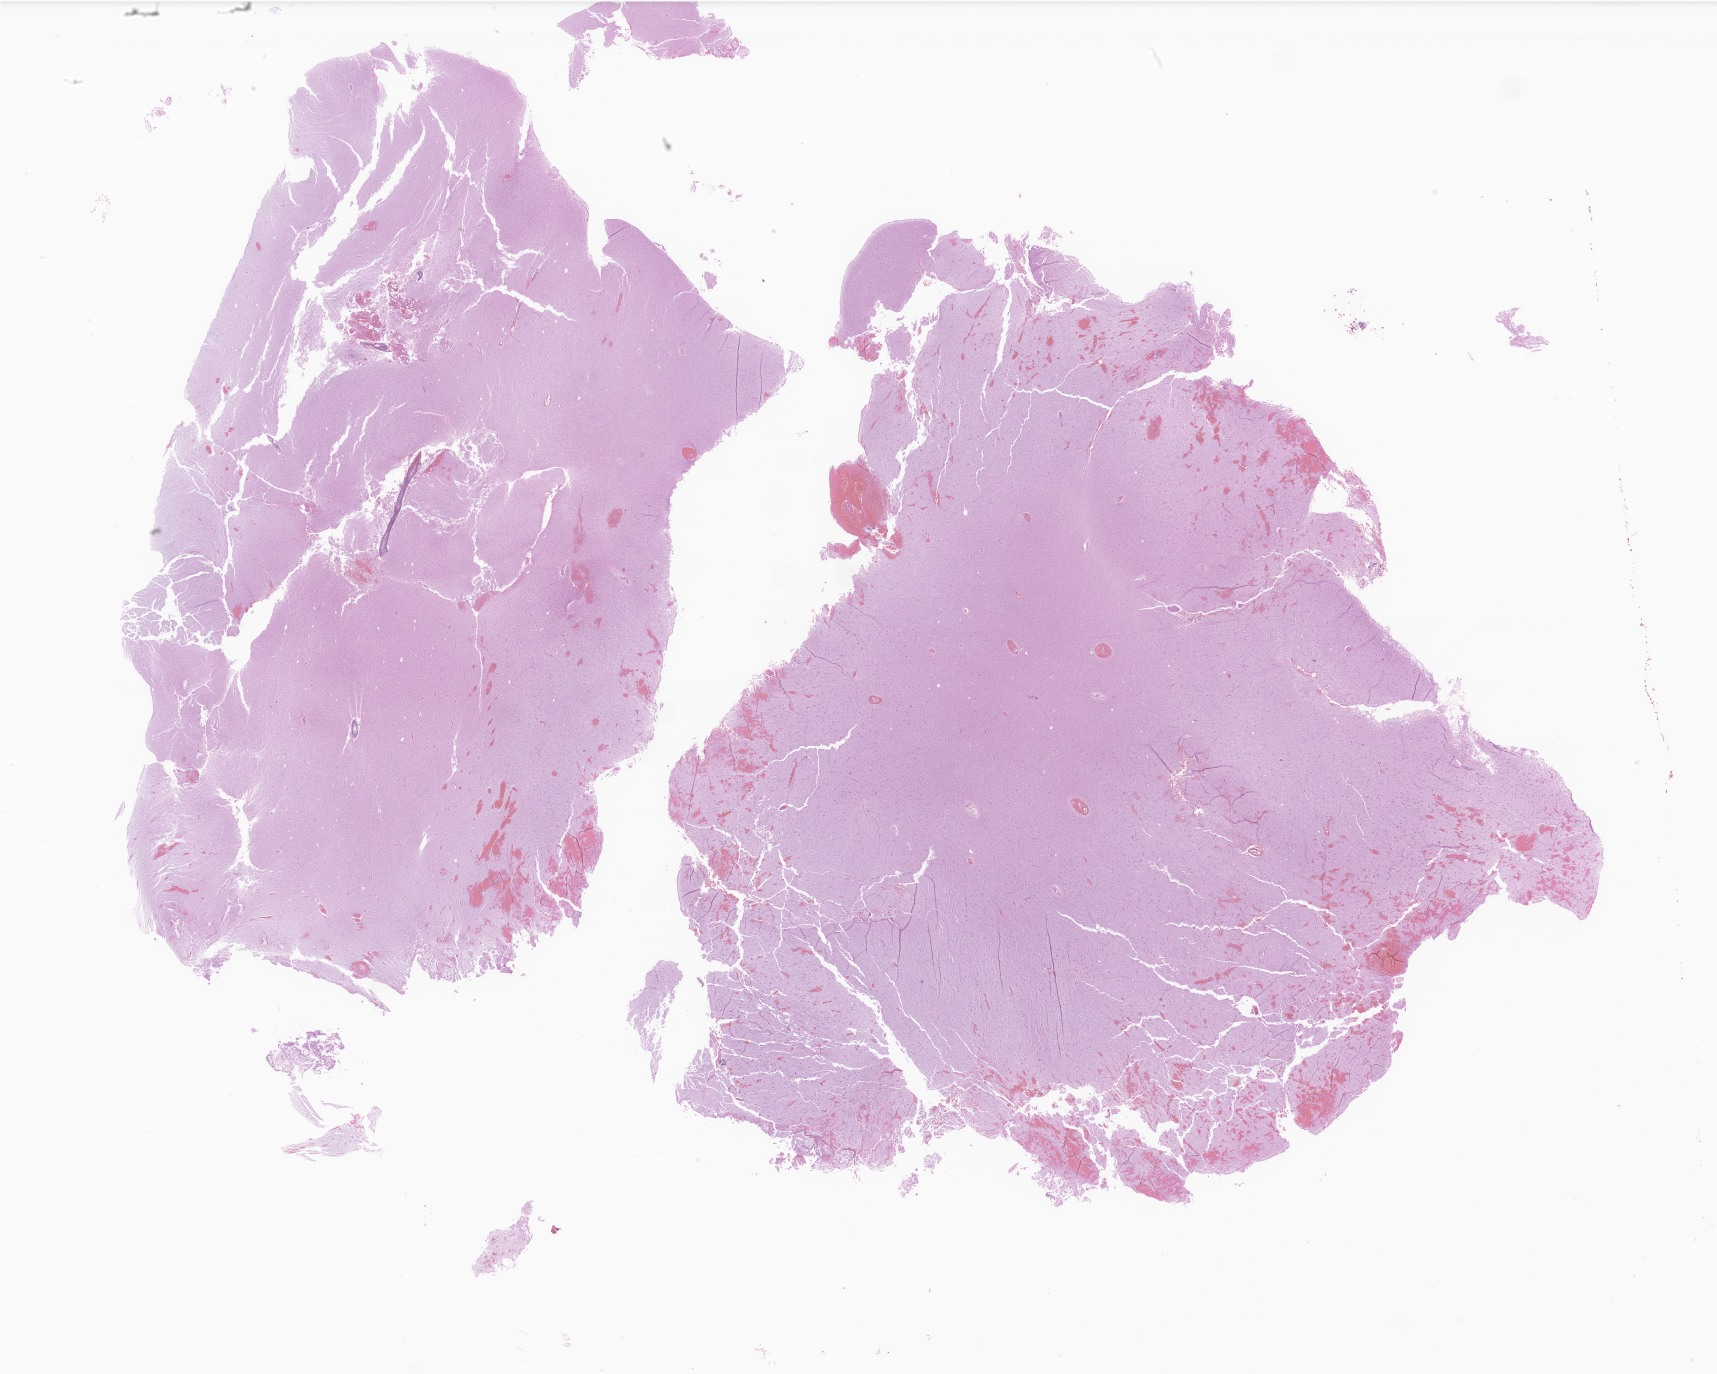
Haematoxylin and eosin whole-slide image of tumor tissue from the brain — whole scanned area (about 29.0 x 23.2 mm) shown as a low-resolution overview. Formalin-fixed, paraffin-embedded (FFPE) tissue. Female patient, age 141 months (11 years 9 months).
Diagnosis (ICD-O-3 morphology term): Oligodendroglioma, NOS.